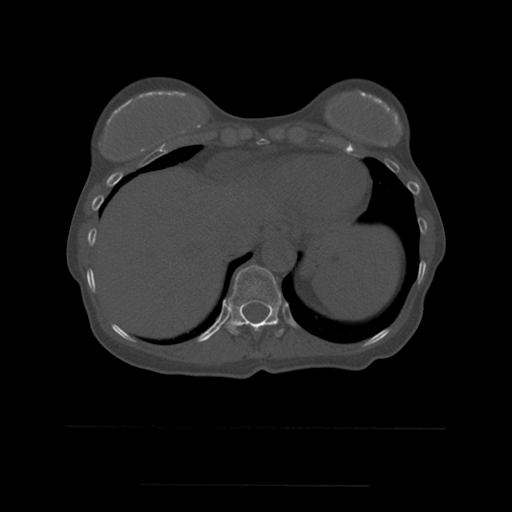
CT including the spine, one axial slice; position 287 of 544 along the scan axis; bone window (W 1800 / L 400 HU); 1.25 mm slice thickness; 512 × 512 image matrix. Patient age 58 years. From the clinical record (not read from this slice): primary cancer: lung.
Structures marked on this image (semi-automatic segmentation, software-assisted and operator-edited):
- T10 vertebra: box from (x=248, y=323) to (x=273, y=332) px
- T11 vertebra: (x=226, y=265)–(x=284, y=337)